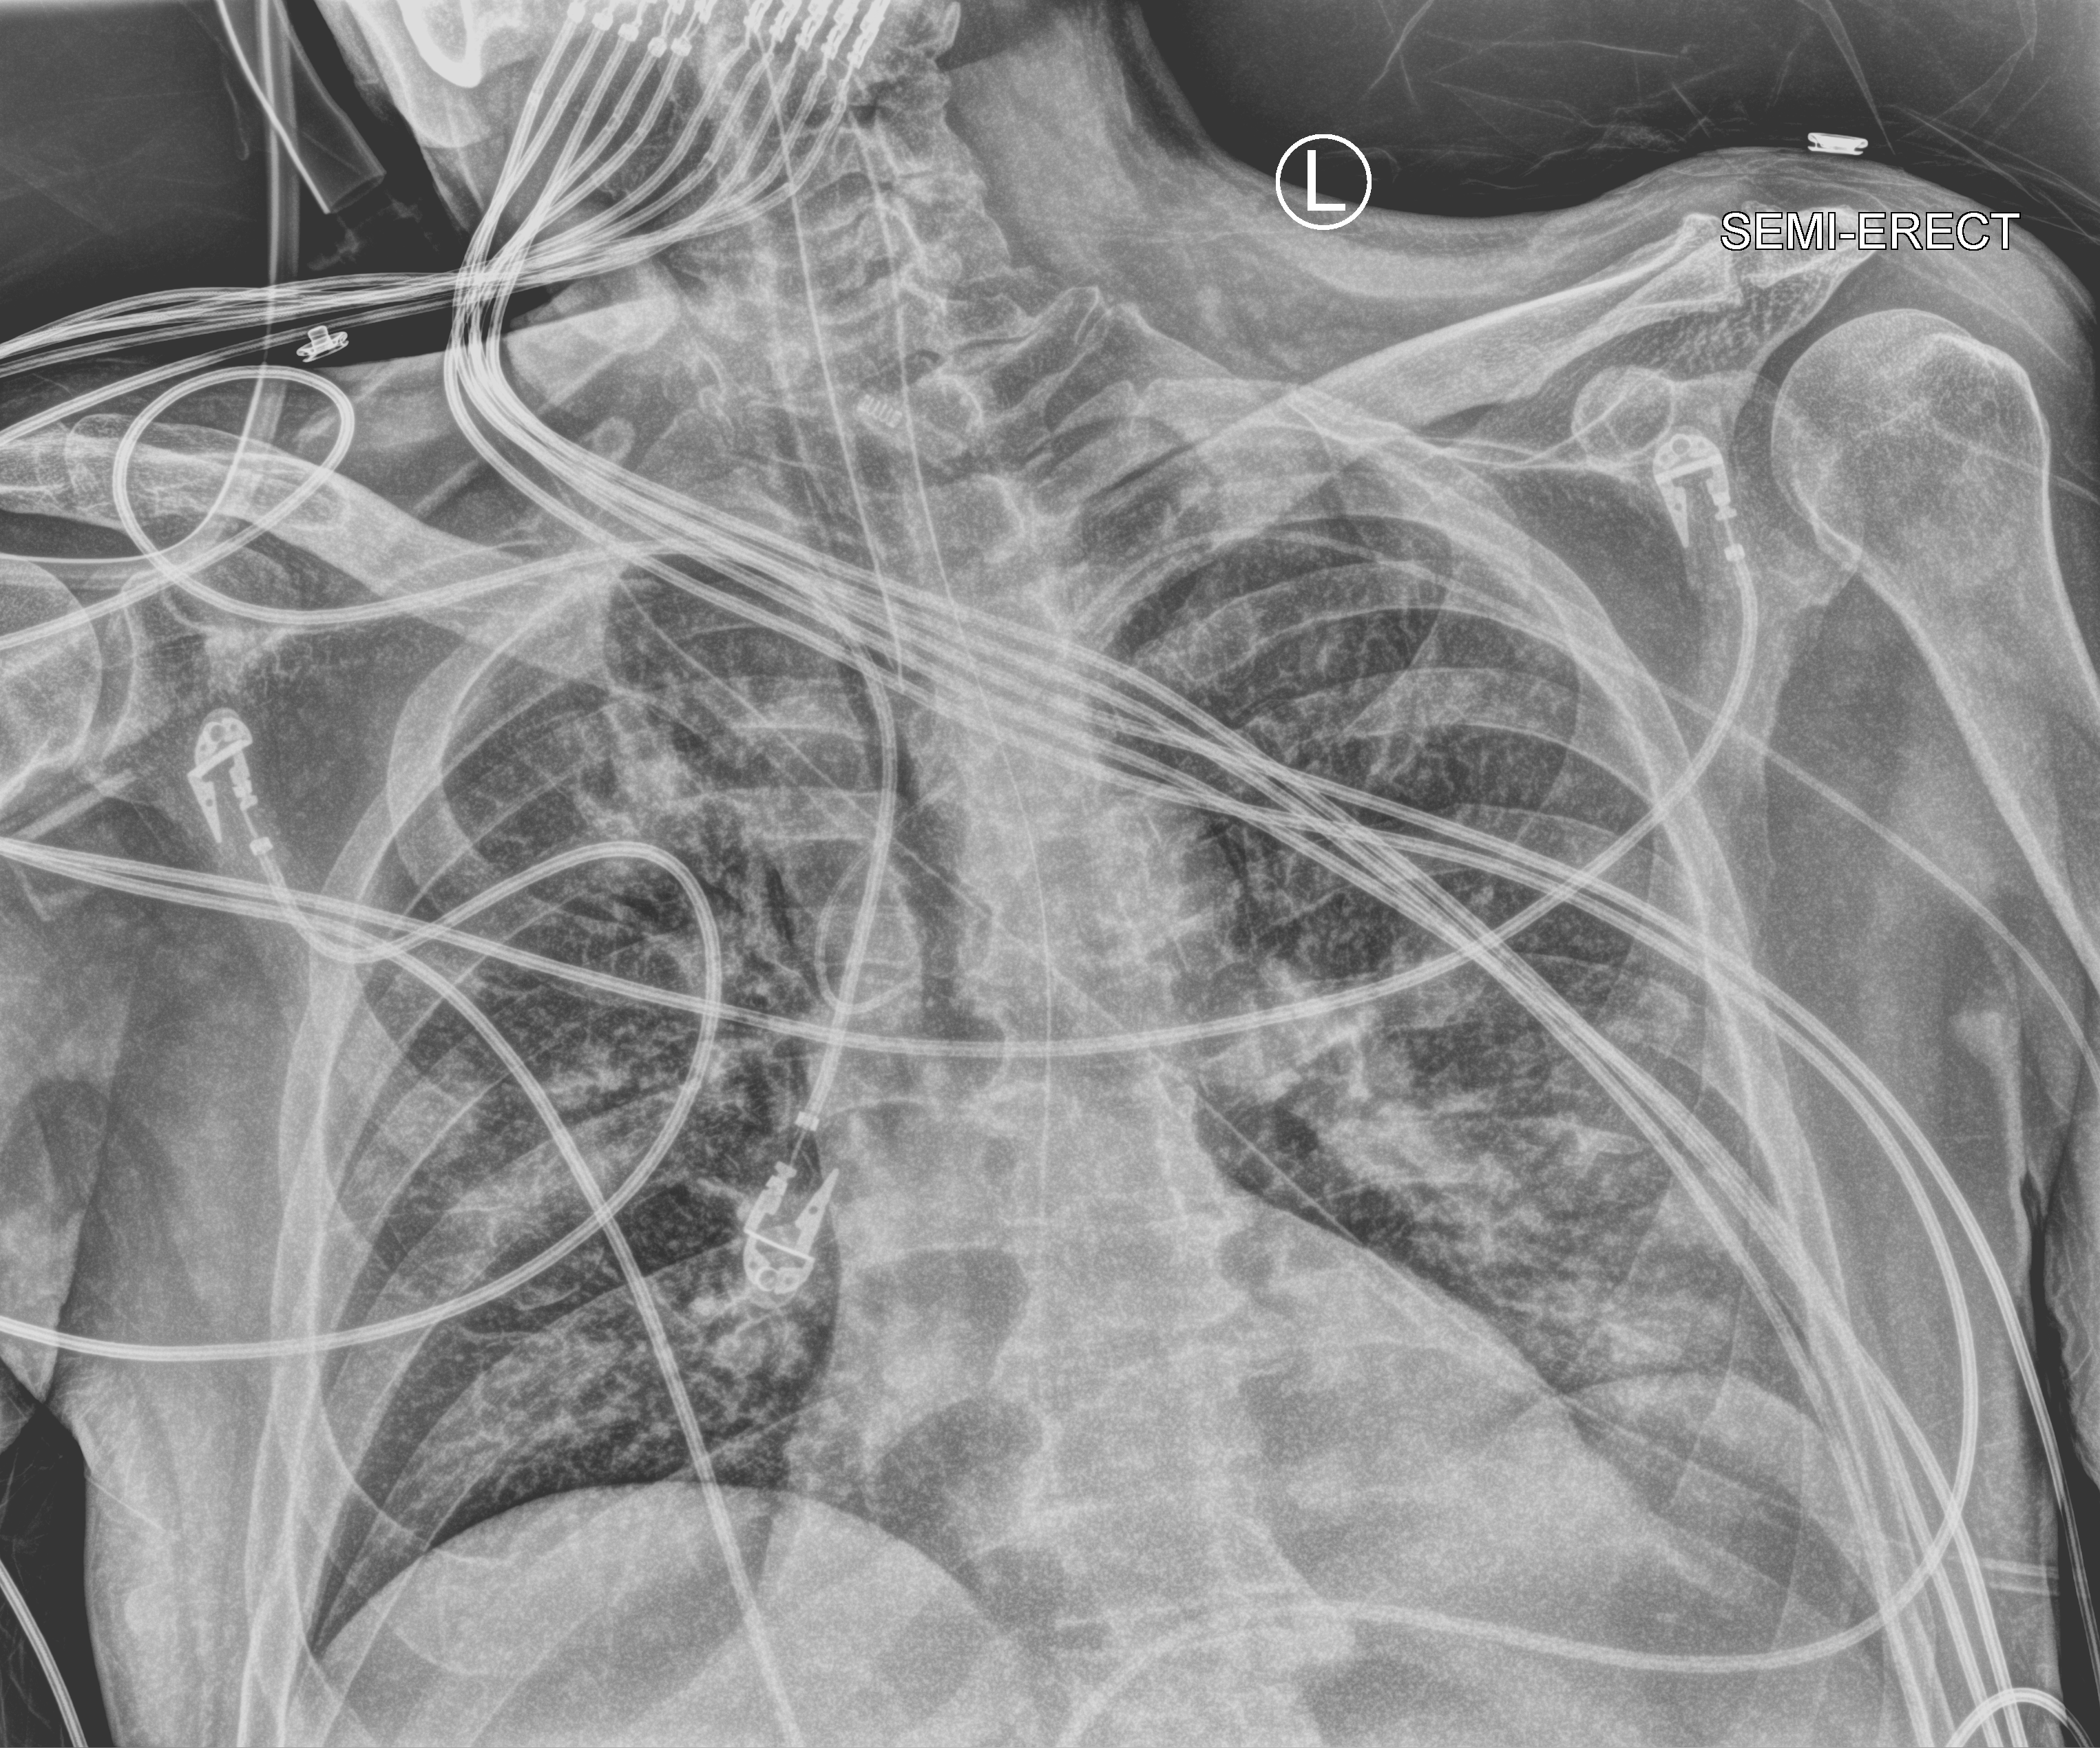
Portable chest radiograph; anteroposterior (AP) projection. Patient hospitalised with COVID-19; male, aged 60–74 years.
Admission-level facts for this patient (not findings on this image; timing relative to this image not recorded): diabetes (admission record): yes; admitted to intensive care during this hospital stay: yes.